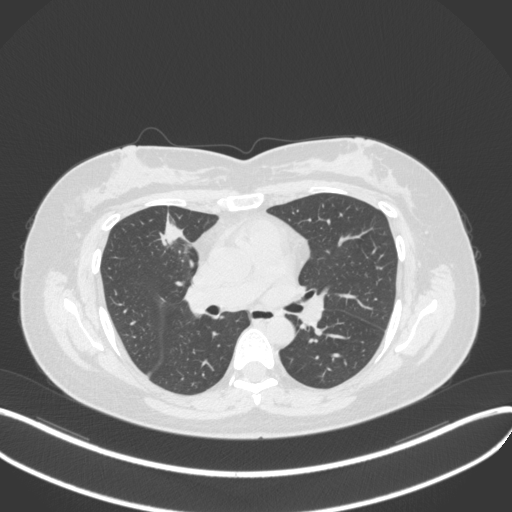
Chest CT, one axial slice. Slice 177 of 272 in the series (ordered by position). Reconstruction kernel B31f. Lung window (W 1500 / L -600 HU). 1 mm slice thickness. 512 × 512 image matrix, field of view 400 × 400 mm. Female patient, age 42 years. Case-level facts recorded for this patient, not image findings: clinical TNM (as recorded): T1b N0 M0.
Outlined on this slice (rectangle marked by the reading radiologist):
- lung tumour (recorded histology: adenocarcinoma): box from (x=157, y=212) to (x=190, y=250) px